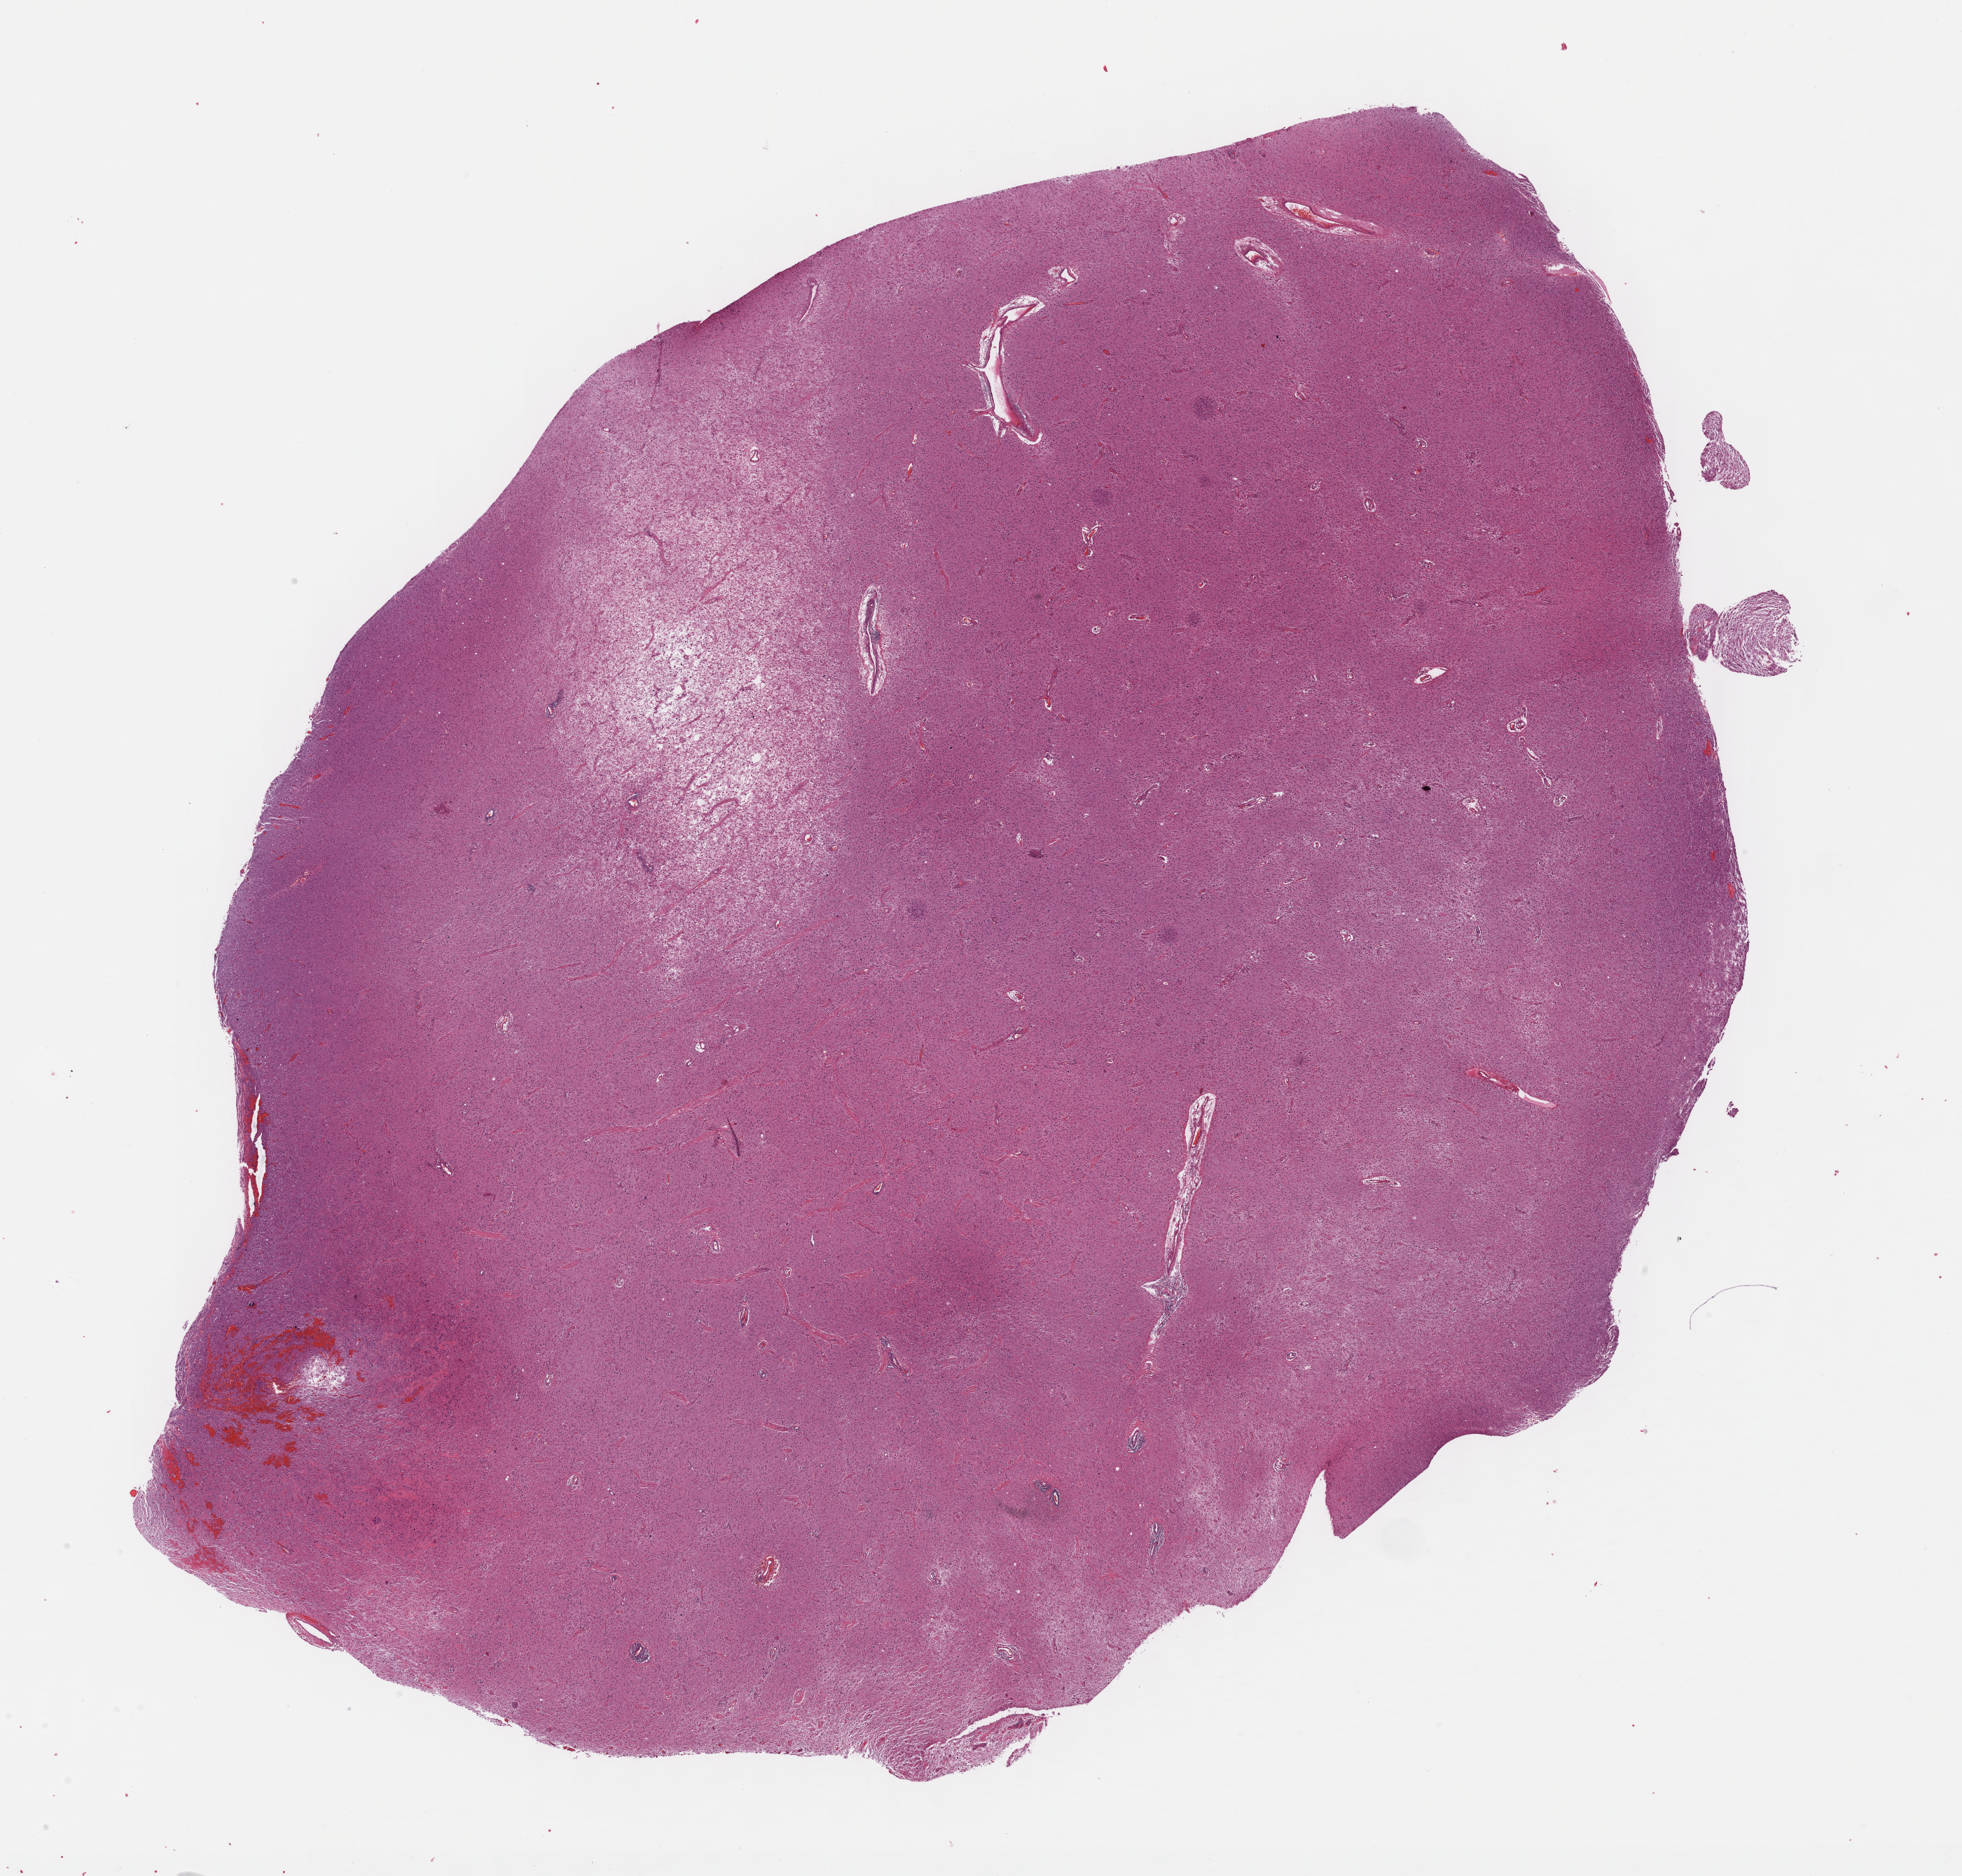
Digitized H&E tissue section (whole slide) — shown as a low-resolution overview of the whole scanned area (about 22.7 x 21.7 mm, slide scanned at 40x); formalin-fixed paraffin-embedded (FFPE) diagnostic section; sample: primary tumour, brain. Male patient; age at initial diagnosis 34 years. Histologic grade: G3 (poorly differentiated).
* laterality: right
* pathologic diagnosis: Mixed glioma (cerebrum)